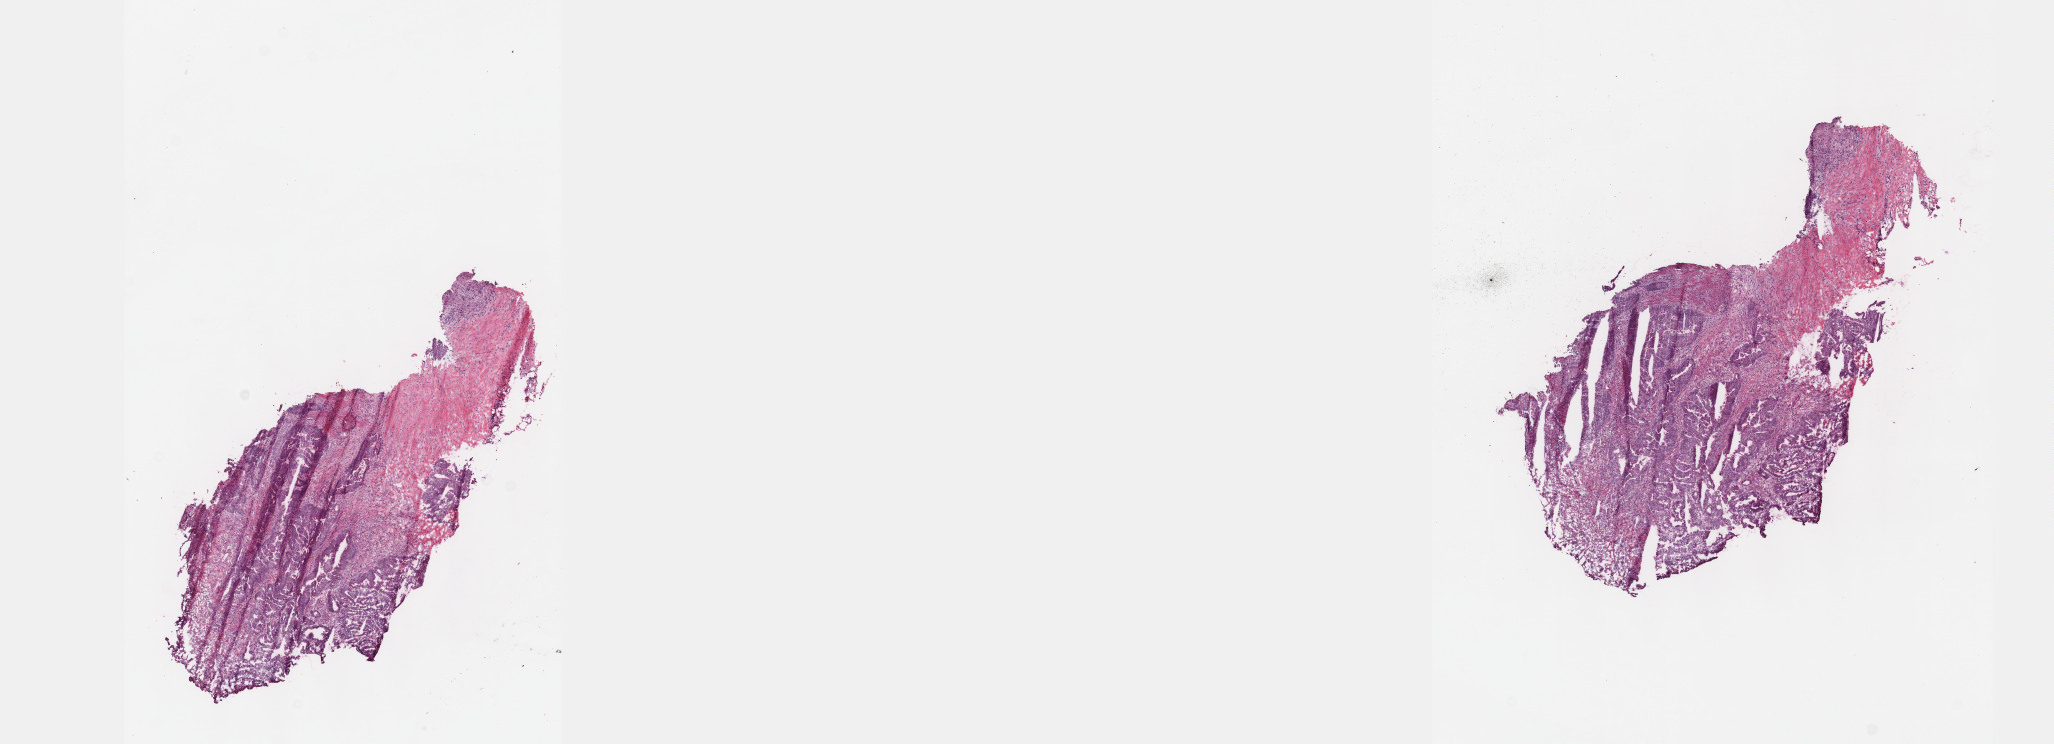
Digitized H&E tissue section (whole slide) — a low-resolution overview of the entire scanned area, about 16.6 x 6.0 mm; frozen section from the bottom of the tissue portion; colon, primary tumour sample. Female patient; age at initial diagnosis 73 years. Pathologist review of this section (percent, as recorded): tumour cells 60%, tumour nuclei 65%, normal cells 0%, stromal cells 32%, necrosis 8%. Inflammatory infiltration, as recorded: lymphocyte infiltration 11%, monocyte infiltration 2%, neutrophil infiltration 7%.
- AJCC pathologic stage: I (5th edition)
- histologic diagnosis: Adenocarcinoma, NOS (sigmoid colon)
- lymph nodes positive (case pathology): 0 of 12 examined